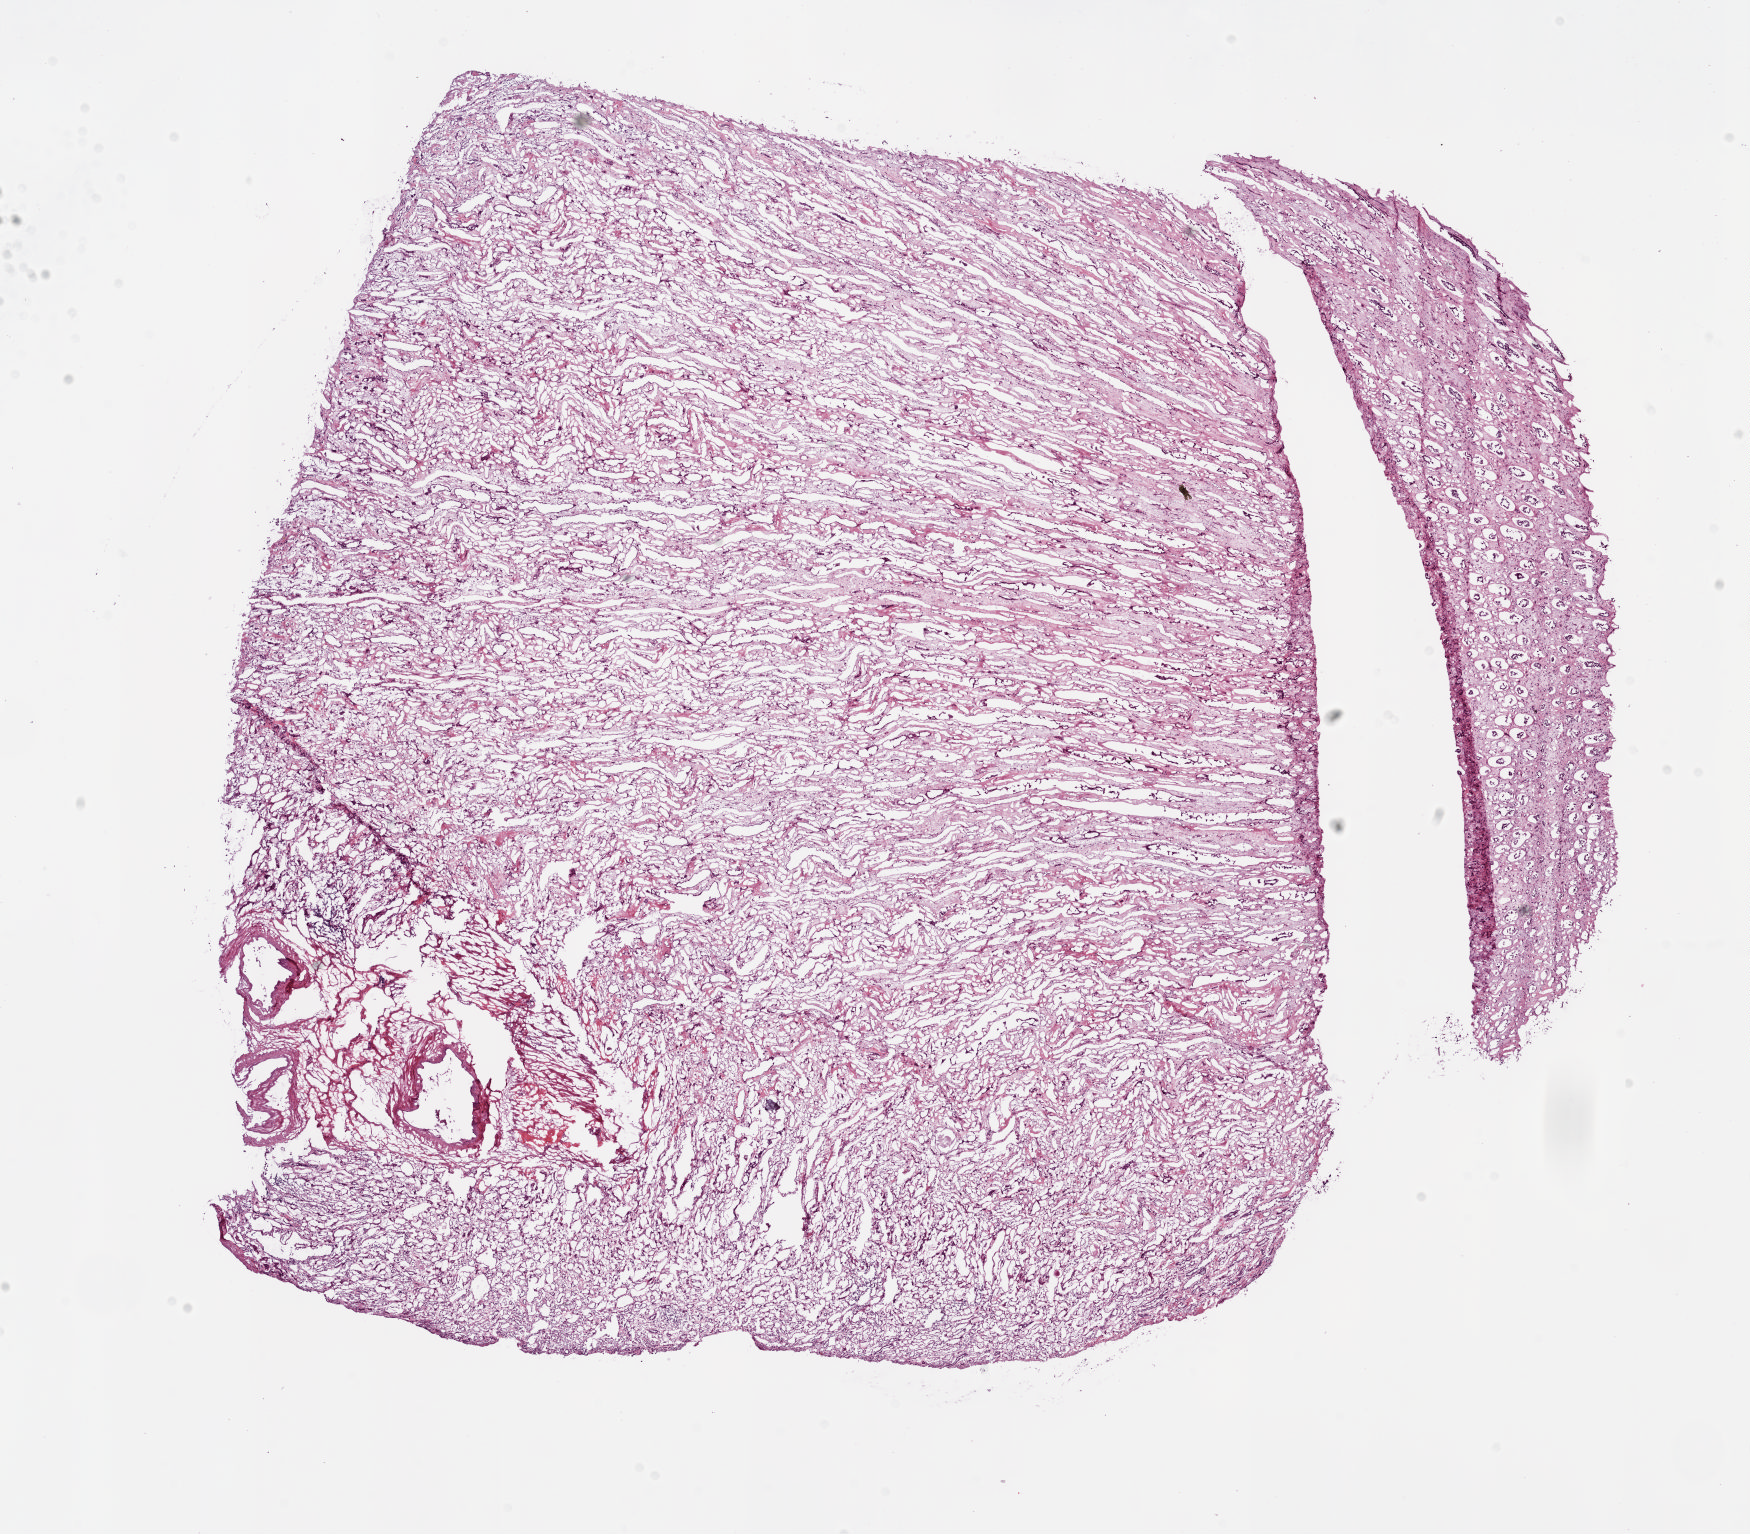
Digitized Hematoxylin and eosin (H&E) stained tissue section (whole slide) — whole scanned area (about 13.9 x 12.2 mm, slide scanned at 20x) shown as a low-resolution overview, frozen section, sample: solid tissue normal (non-tumour tissue), kidney. Patient: female, age at initial diagnosis 75 years.
This section: solid tissue normal sample (biorepository sample class). Patient diagnosis: Clear cell adenocarcinoma, NOS.